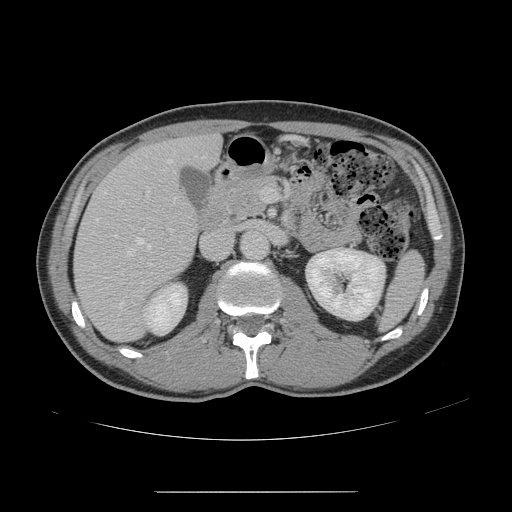
Contrast-enhanced abdominal CT, one axial slice. Position 75 of 178 along the scan axis. Intravenous contrast given. Soft-tissue window (W 400 / L 40 HU). 2.5 mm slice thickness. 512 × 512 image matrix, field of view 401 × 401 mm. Male patient, age 53 years. From the clinical record (not read from this slice): diagnosis: colorectal cancer liver metastases, imaged before liver resection; multiple liver metastases: yes; largest metastasis: 2.4 cm; chemotherapy before resection: yes.
Outlined on this slice (outlined manually by an expert reader):
- hepatic veins: bounding box [x1, y1, x2, y2] px = [94, 159, 172, 309]
- liver: [74, 136, 221, 342]
- planned liver remnant (the part of the liver to remain after resection): [176, 136, 220, 164]
- portal vein (with intrahepatic branches): [147, 187, 267, 202]